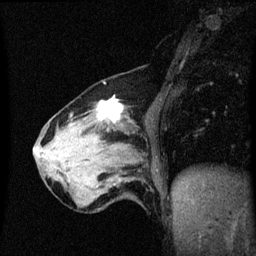
Breast MRI (dynamic contrast-enhanced), one sagittal slice; slice 20 of 60 in the series (ordered by position); dynamic contrast-enhanced series, image 2 of 3 at this slice position (ordered by acquisition); 1.5 T; TE 4.2 ms, TR 8.4 ms; 2 mm slice thickness; 256 × 256 image matrix, field of view 200 × 200 mm. Female patient, age 64 years. Case-level facts recorded for this patient, not image findings: setting: breast cancer imaged before/during neoadjuvant chemotherapy; receptor status: HR-positive, HER2-negative.
Annotated regions visible in this slice (semi-automatically segmented with operator editing):
- analysis volume of interest (the breast-tissue region the enhancement analysis was run in; not a lesion): bounding box (x1, y1, x2, y2) in pixels: (56, 96, 142, 175)
- tumour enhancement mask (voxels above the 70 % enhancement threshold inside the analysis volume of interest): (99, 98, 124, 121)